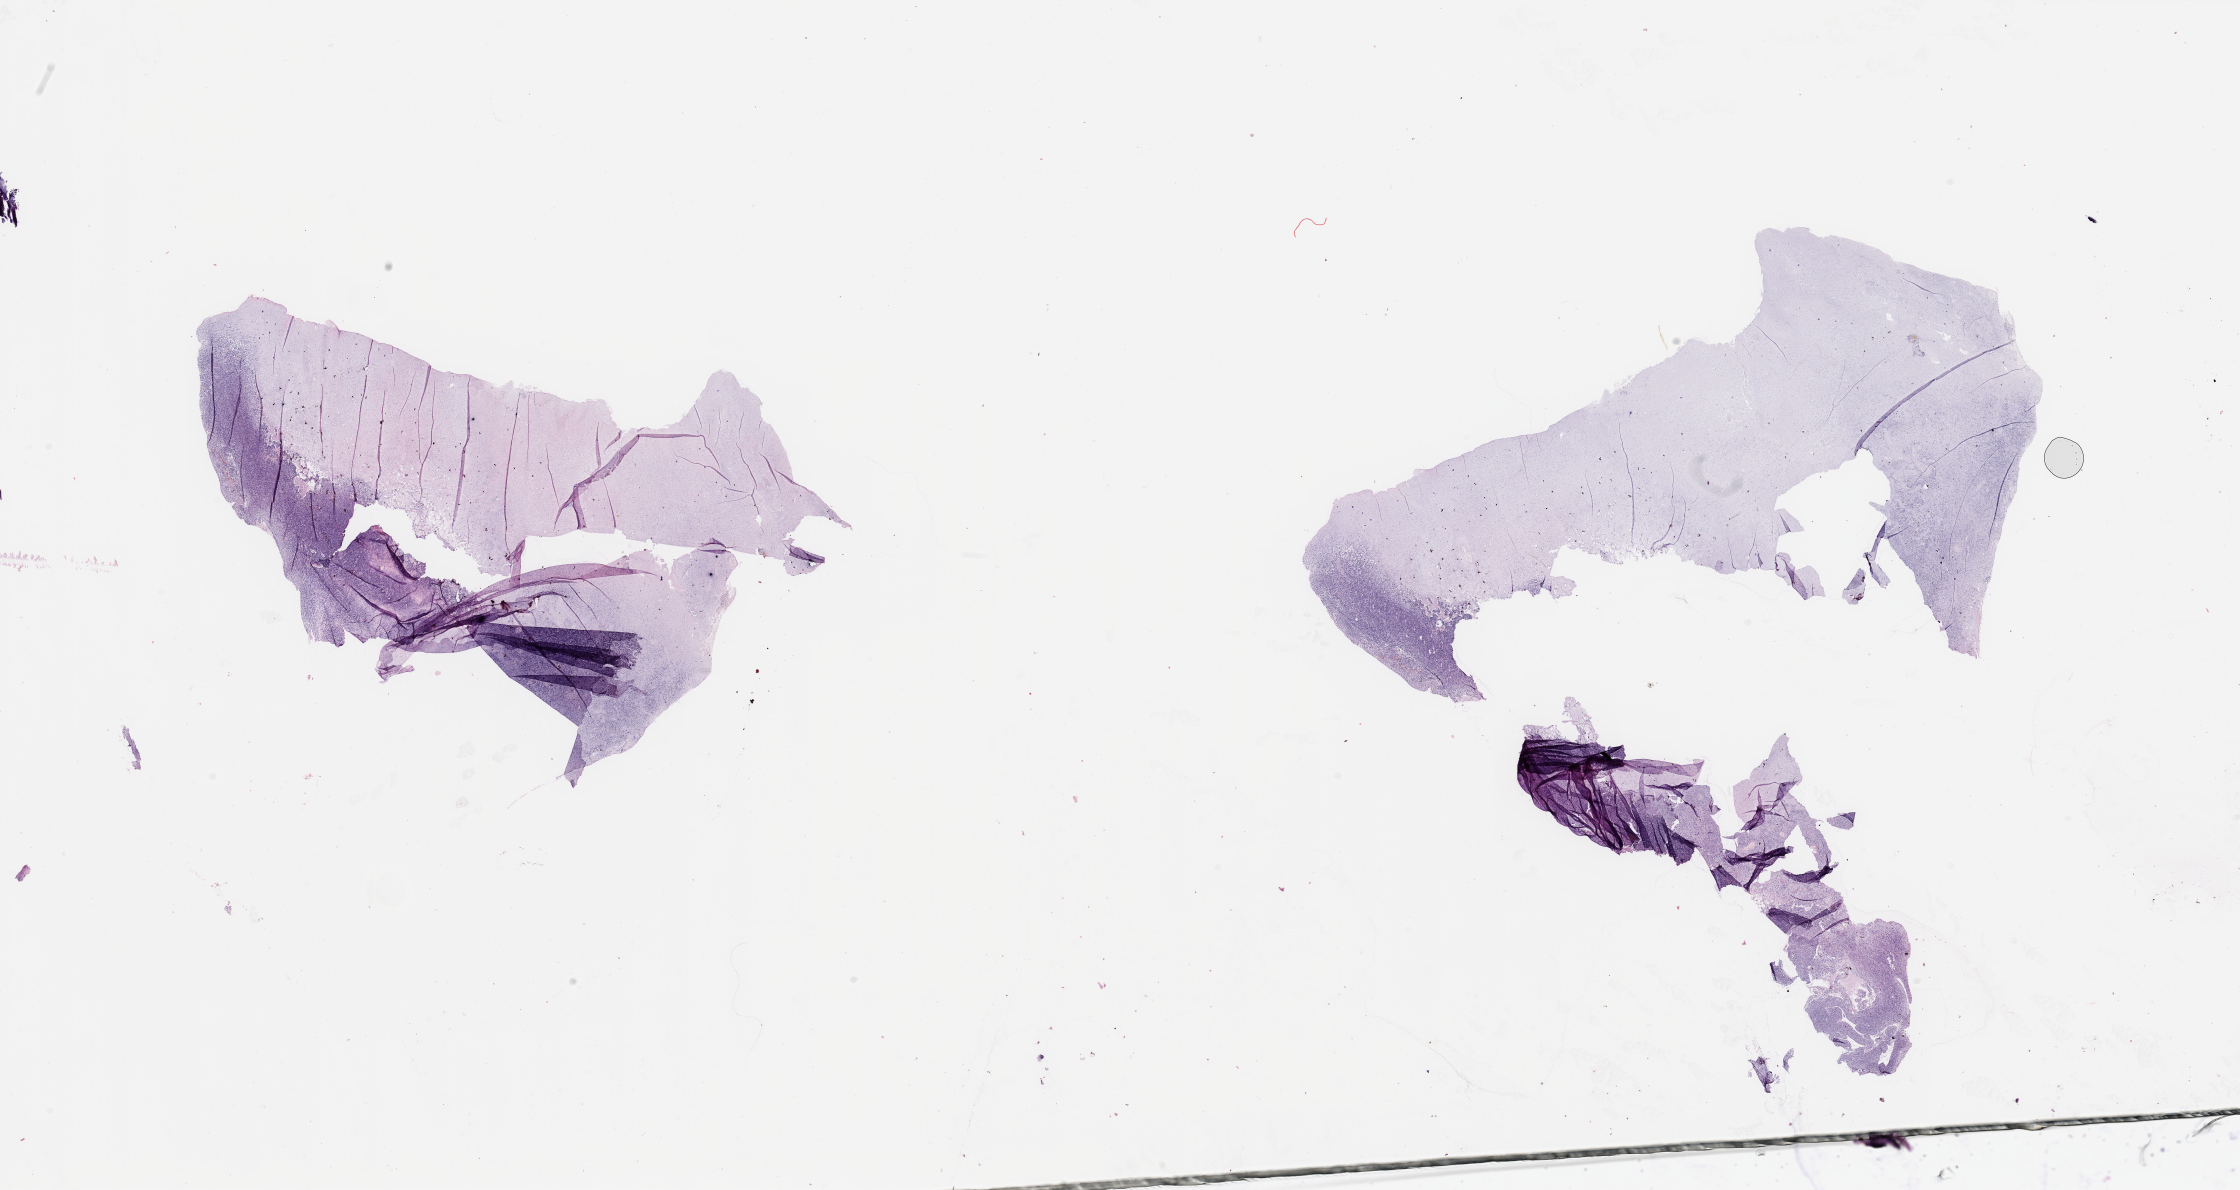
Whole-slide histology image, Hematoxylin and eosin (H&E) stained, low-resolution overview of the scanned area, about 35.4 x 18.8 mm (acquisition: 20x scan), tumour tissue sample, brain. Male, 81 y/o.
Diagnosis: Glioblastoma. Primary tumour site (as recorded): temporal lobe.